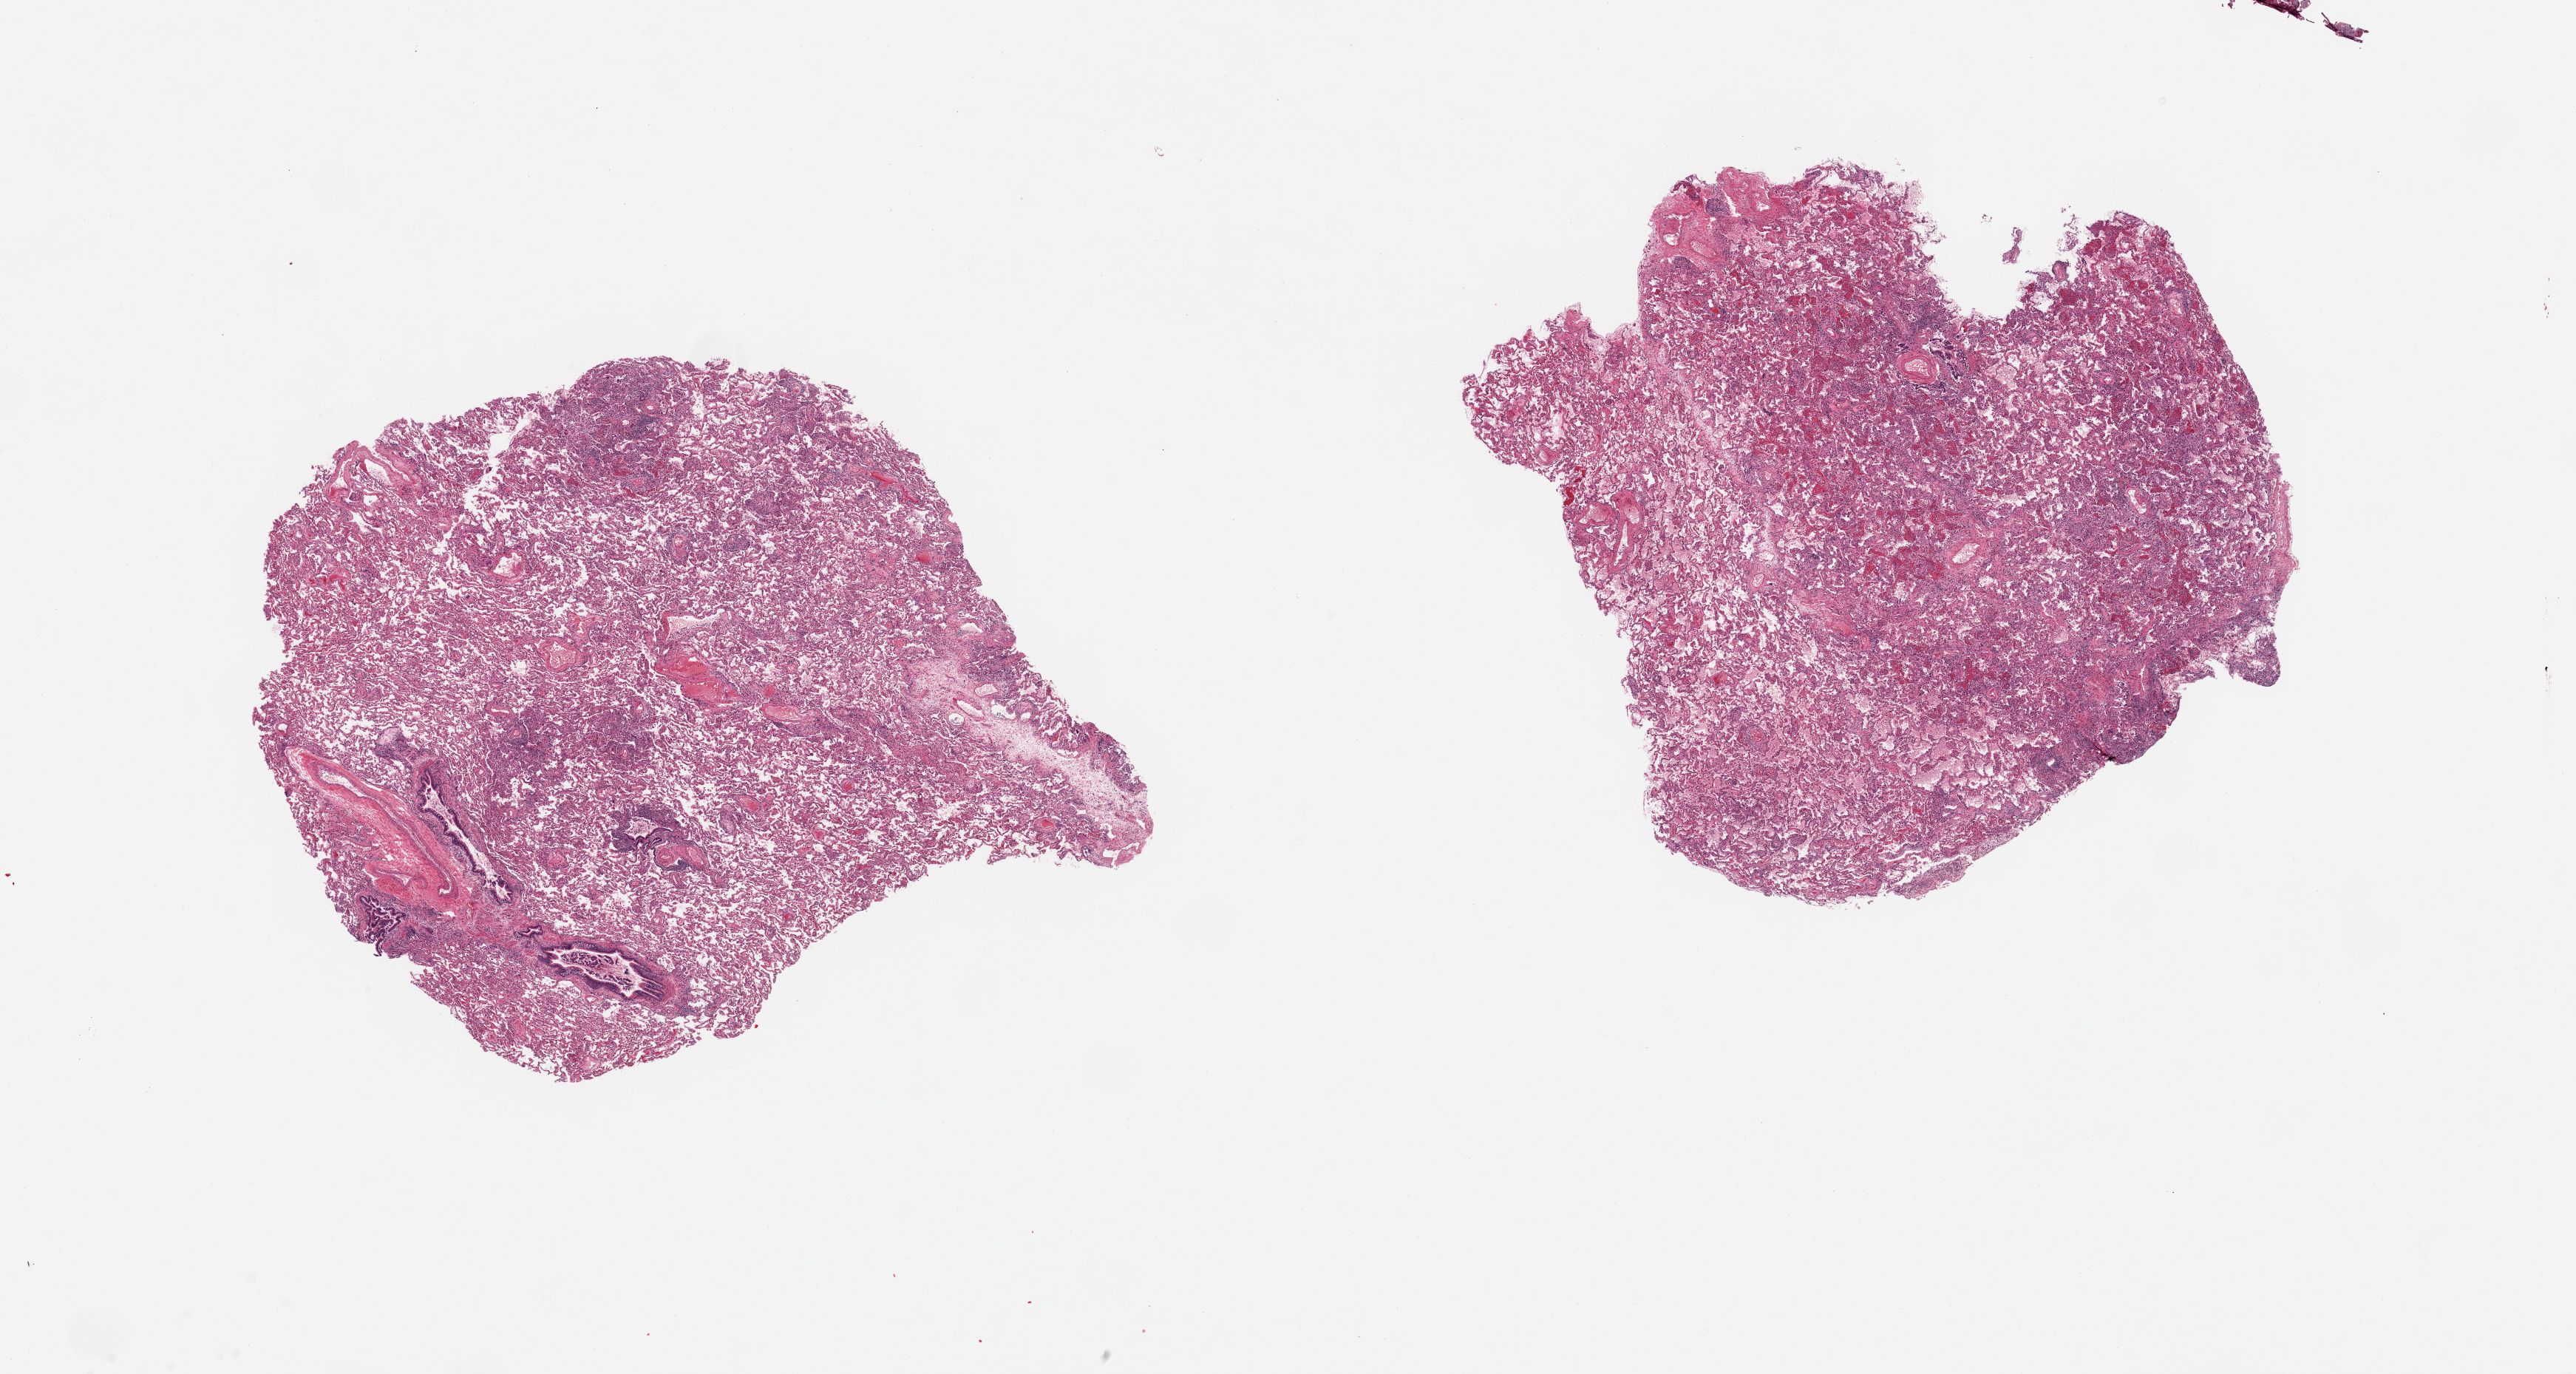
Hematoxylin and eosin (H&E) whole-slide image, a low-resolution overview of the entire scanned area, about 27.6 x 14.7 mm (acquisition: 20x scan), PAXgene-fixed, paraffin-embedded tissue, section of lung (target tissue), donor tissue sample. Male donor.
Reviewer comment on this tissue sample: 2 pieces patchy chronic and acute bronchitis/peribronchial pneumonitis.